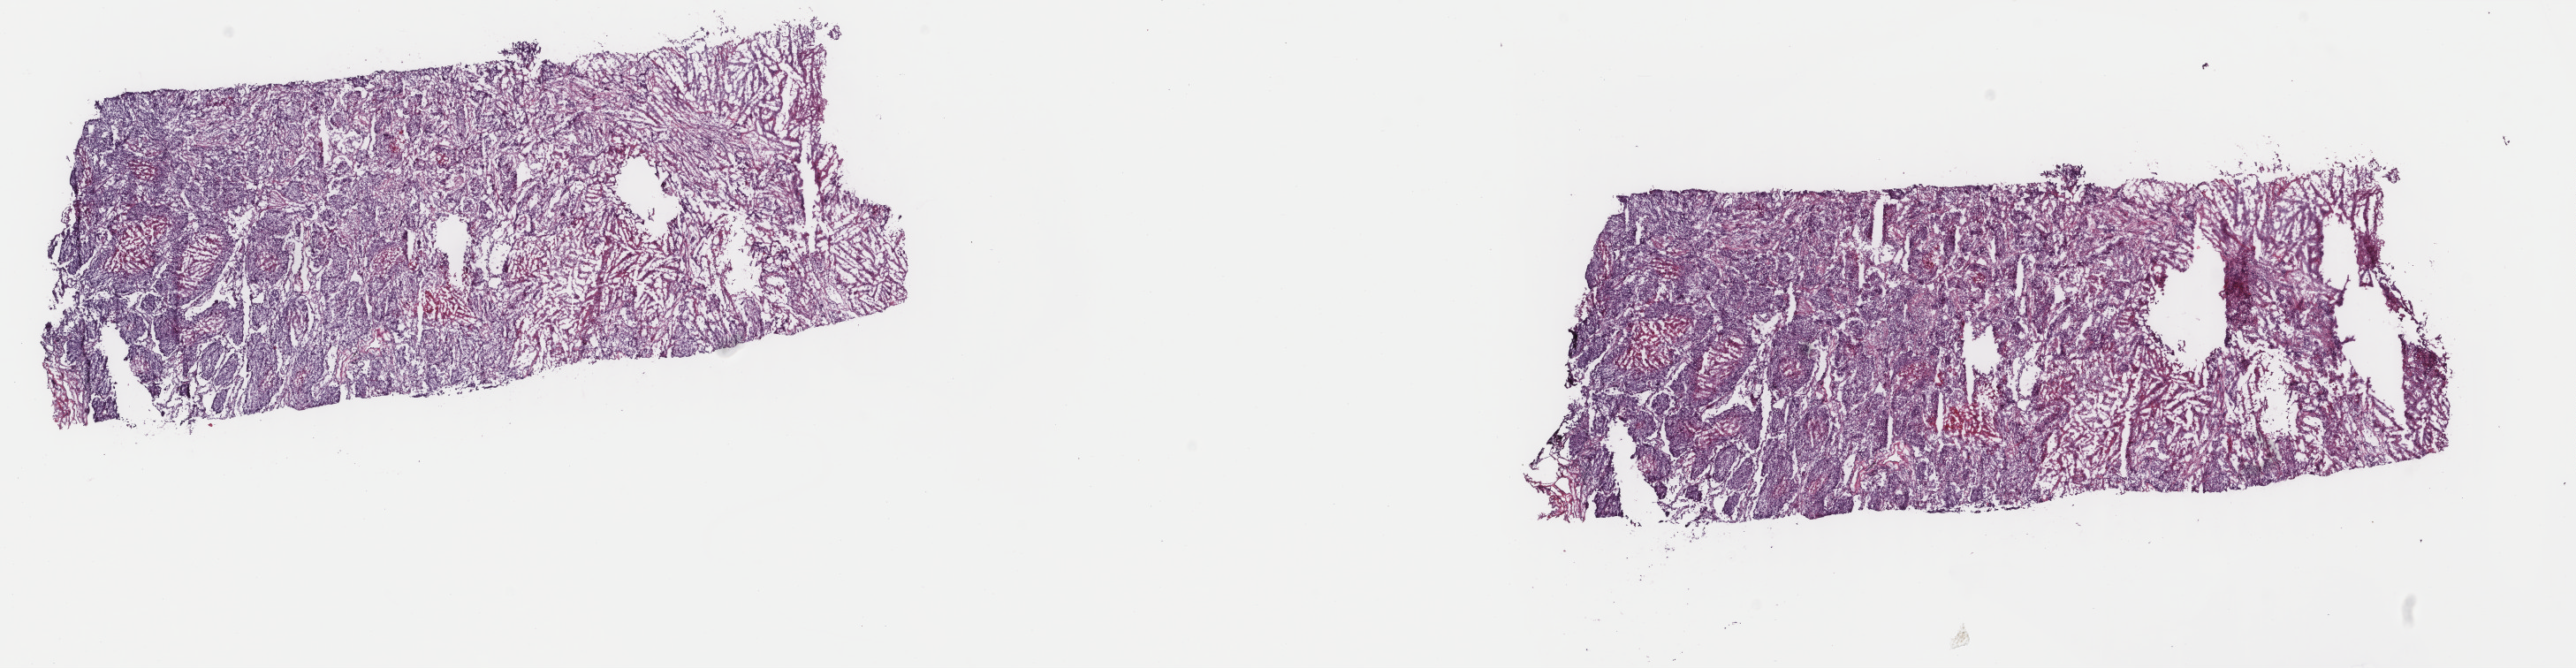
Digitized H&E-stained tissue section (whole slide), shown as a low-resolution overview of the whole scanned area (about 23.1 x 6.0 mm, from a 40x scan); frozen section from the top of the tissue portion; sample: primary tumour, lung. Female patient; age at initial diagnosis 74 years. Pathologist review of this section (percent, as recorded): tumour cells 80%, tumour nuclei 77%, normal cells 0%, stromal cells 0%, necrosis 20%. Inflammatory infiltration, as recorded: lymphocyte infiltration 0%, monocyte infiltration 0%, neutrophil infiltration 0%.
AJCC pathologic stage: IB. Diagnosis: Squamous cell carcinoma, NOS (lower lobe, lung).